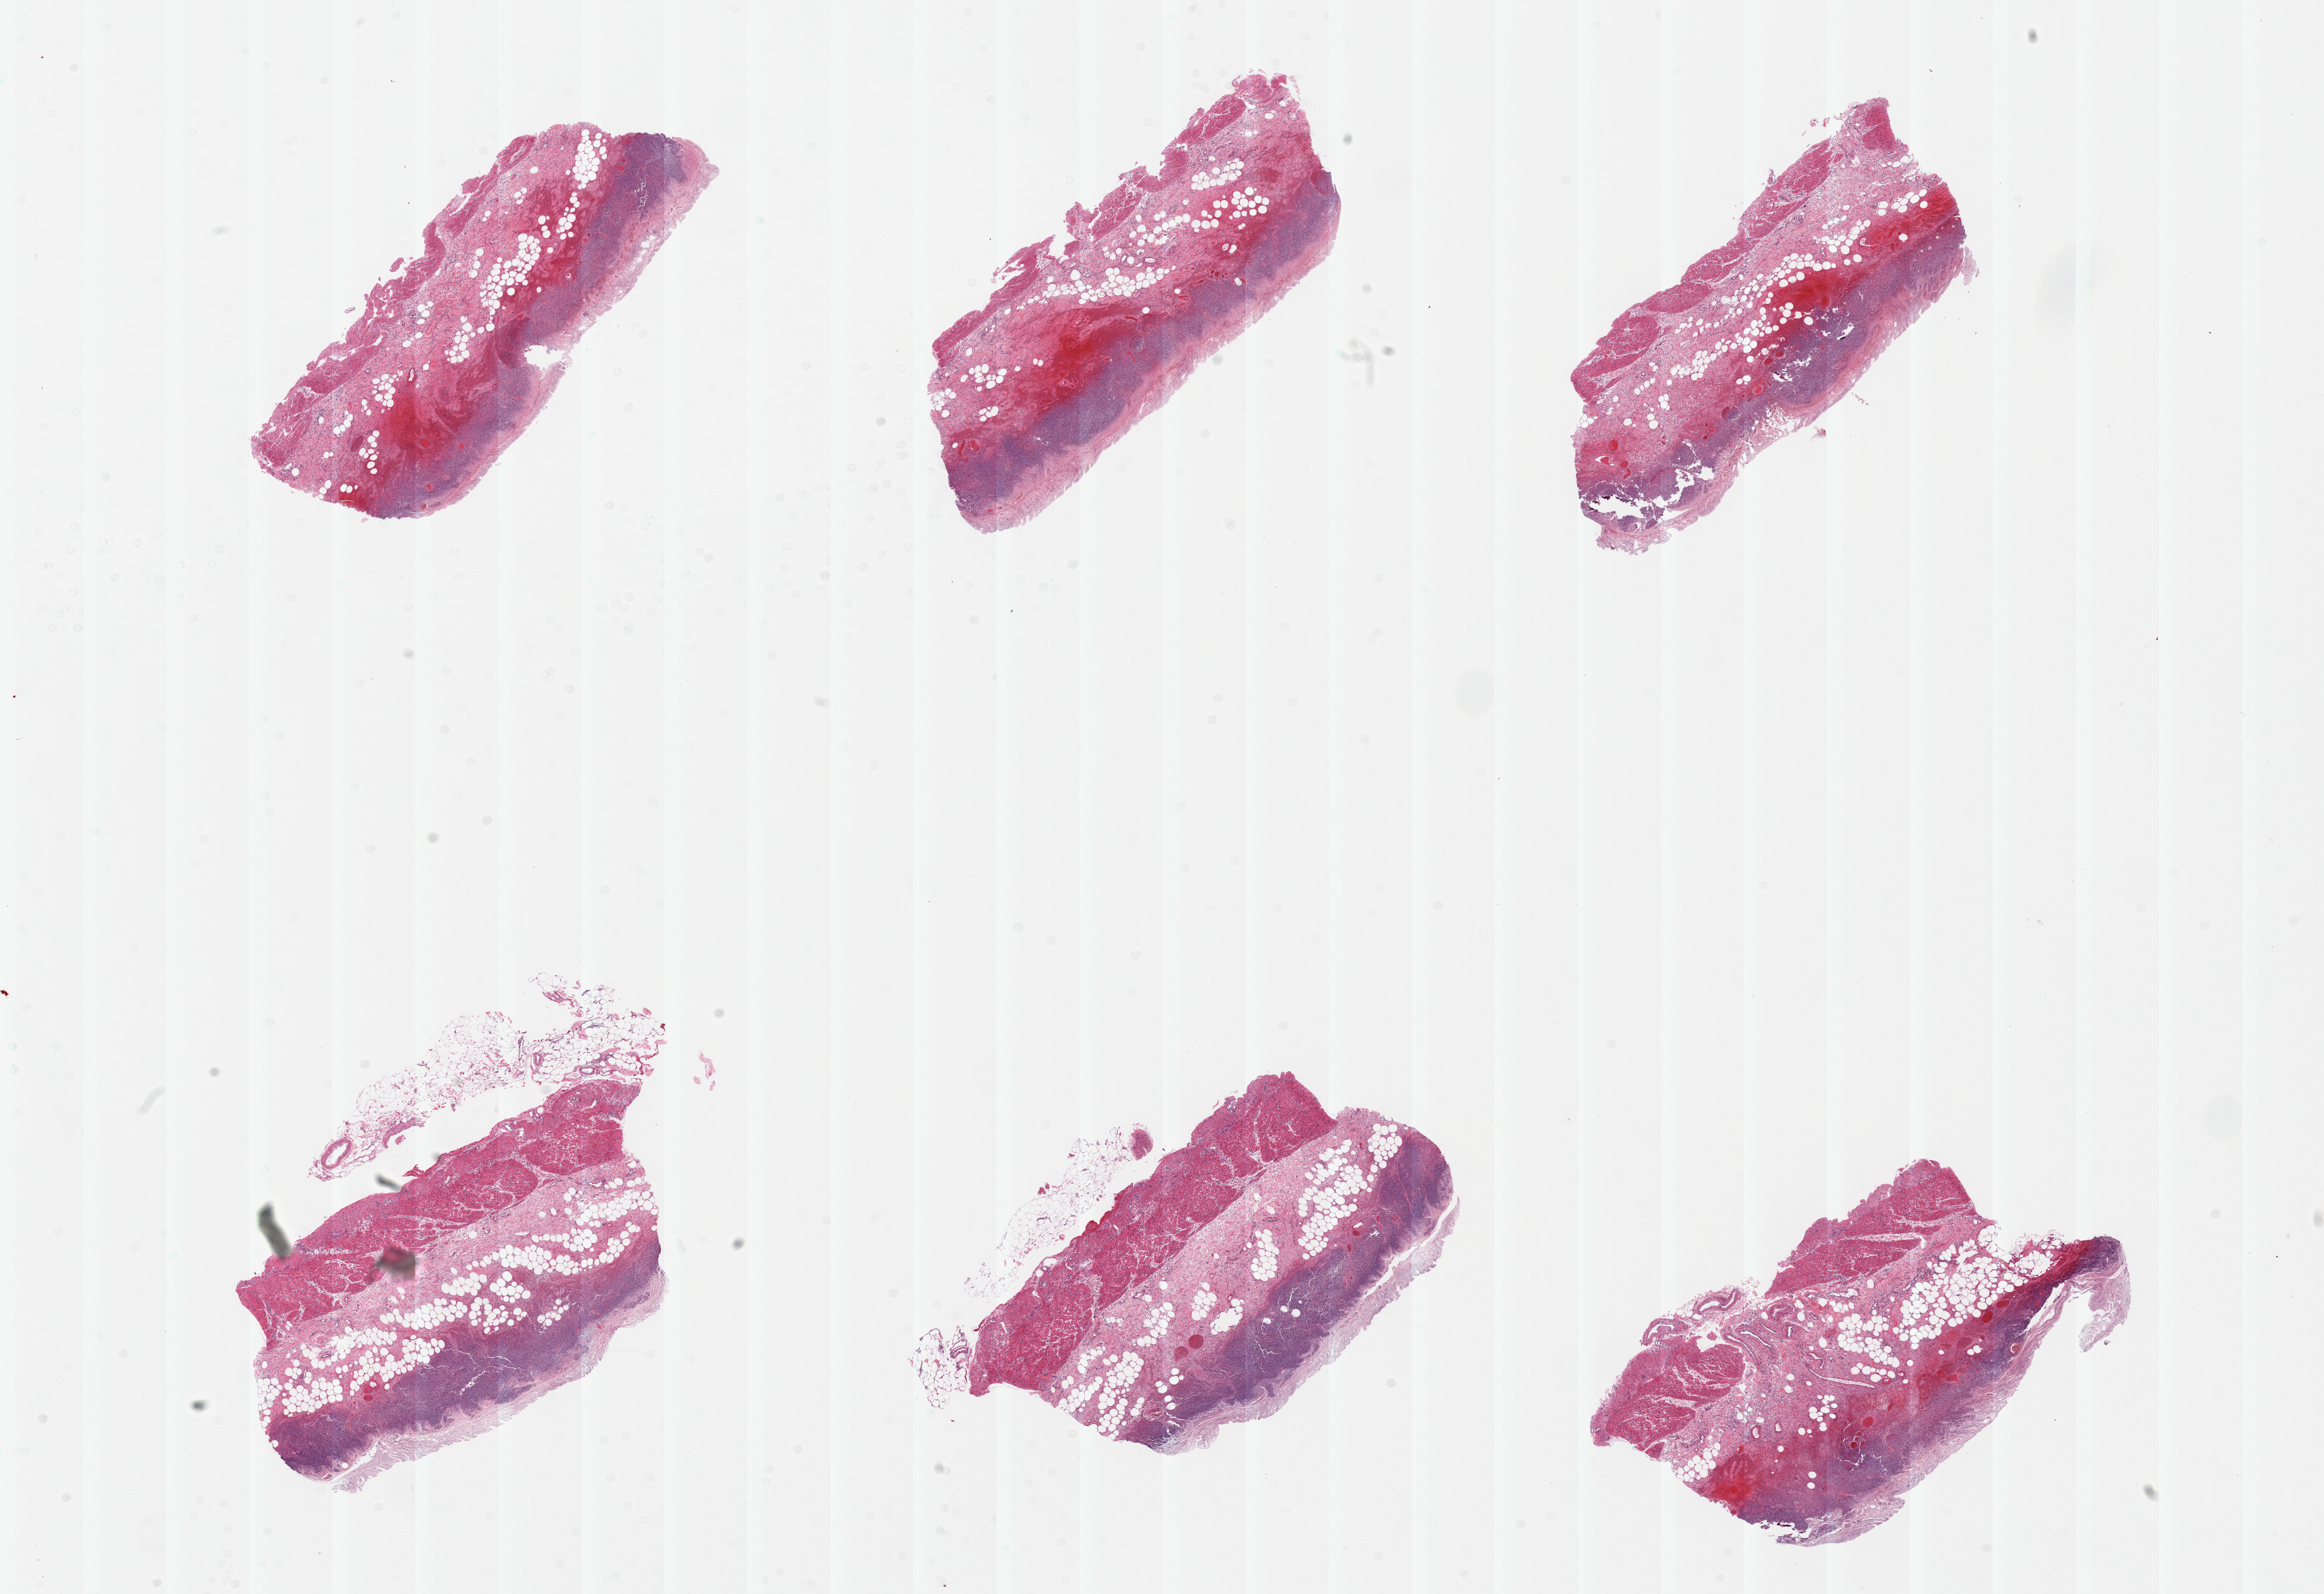
Digitized H&E-stained section, whole scanned area (about 27.6 x 18.9 mm) shown as a low-resolution overview. PAXgene-fixed, paraffin-embedded tissue. Section of transverse colon (target tissue). Tissue donor sample.
• review note (as recorded): 6 pieces, extensive mucosal necrosis and hemorrhage c/w history of ulcerative colitis